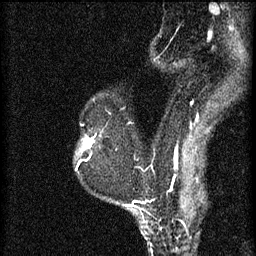
Breast MRI (dynamic contrast-enhanced), one sagittal slice; slice 46 of 60 in the series (ordered by position); 3 images stored at this slice position (order not interpretable as contrast timing); 1.5 T; TE 4.2 ms, TR 8.2 ms; 2 mm slice thickness; 256 × 256 image matrix, field of view 180 × 180 mm. Patient: female, 60 years.
Annotated regions visible in this slice (semi-automatic segmentation, software-assisted and operator-edited):
- analysis volume of interest (the breast-tissue region the enhancement analysis was run in; not a lesion): bounding box (x1, y1, x2, y2) in pixels: (74, 134, 97, 159)
- tumour enhancement mask (voxels above the 70 % enhancement threshold inside the analysis volume of interest): (84, 134, 97, 149)